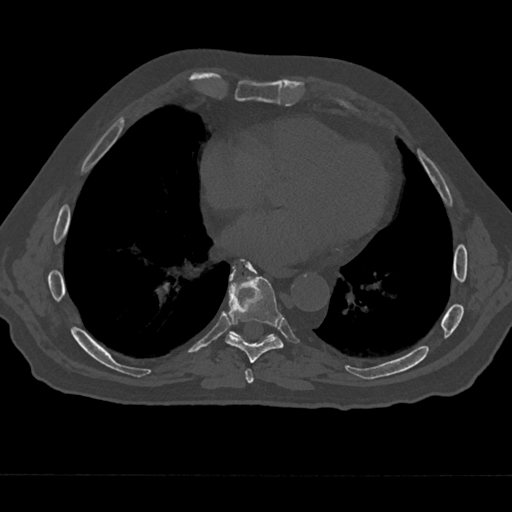
CT including the spine, one axial slice; position 305 of 797 along the scan axis; reconstruction kernel Br40s/3; 120 kVp; bone window (W 1800 / L 400 HU); 0.5 mm slice thickness; 512 × 512 image matrix, field of view 377 × 377 mm. Male patient, age 75 years. From the clinical record (not read from this slice): primary cancer: renal; vertebrae with lytic lesions (as recorded): T4.
Structures marked on this image (semi-automatically segmented with operator editing):
- T7 vertebra: bounding box (x1, y1, x2, y2) in pixels: (241, 367, 255, 384)
- T8 vertebra: (225, 262, 284, 363)
- T9 vertebra: (230, 261, 274, 337)